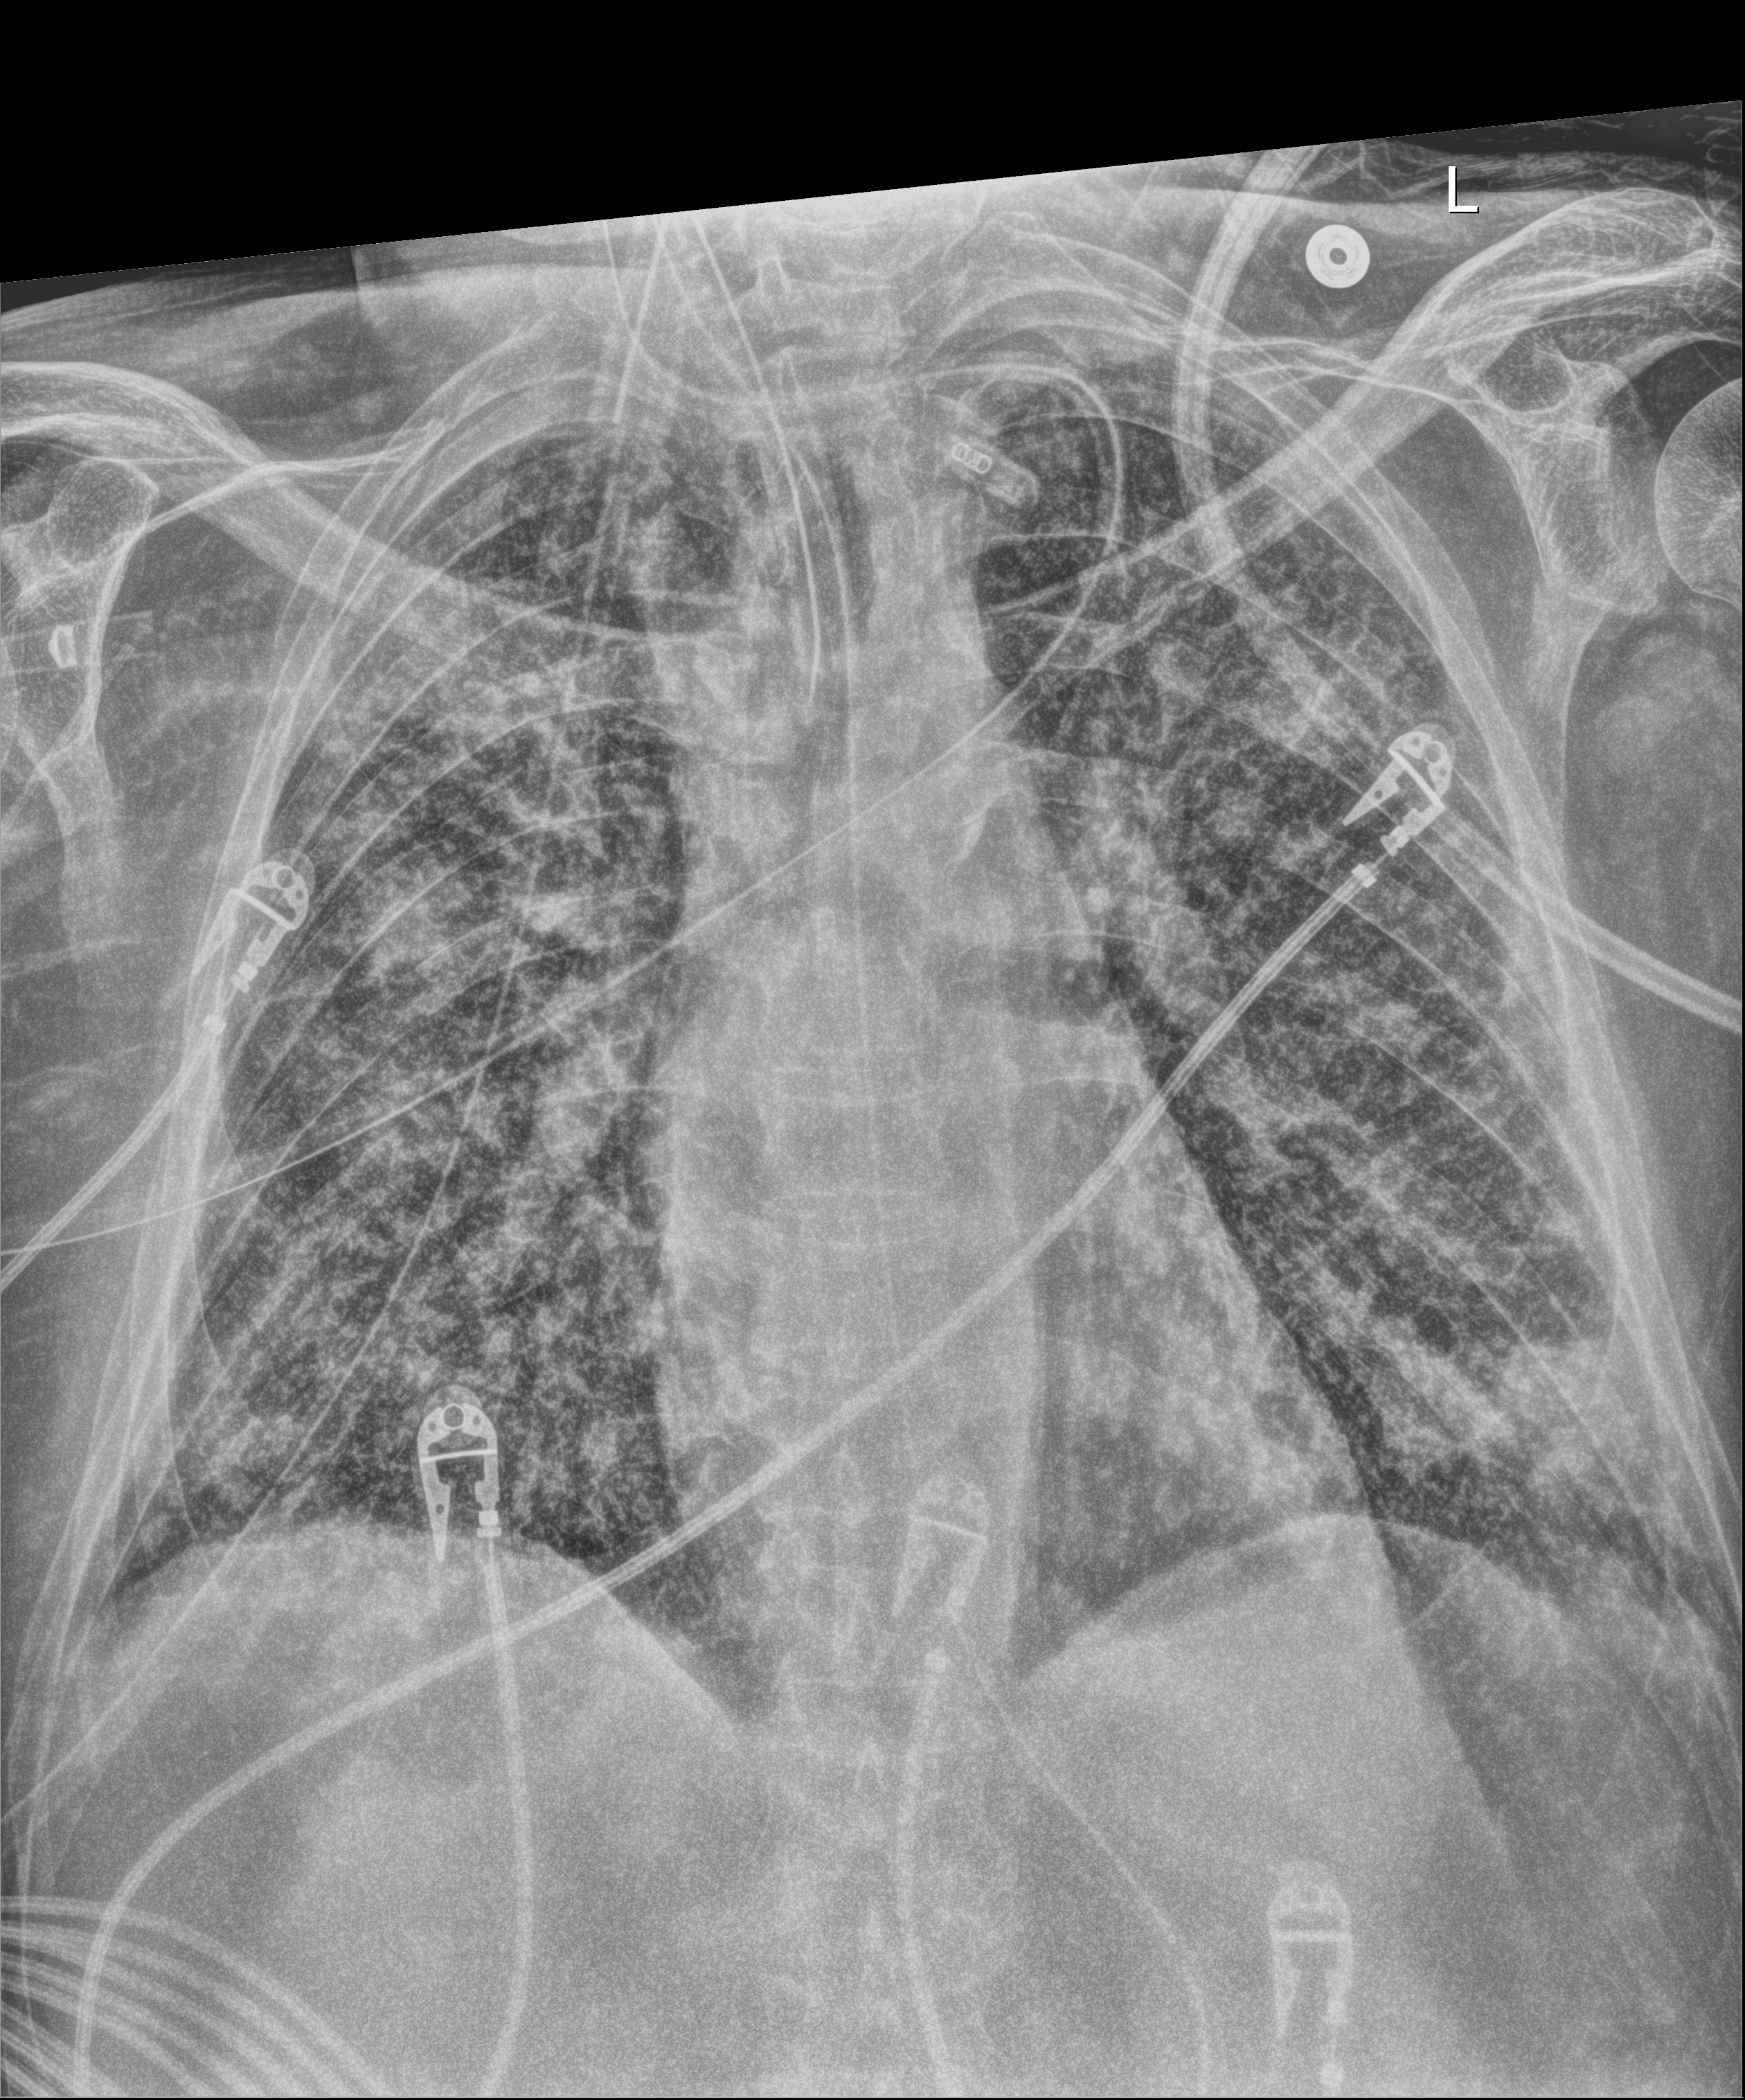
Chest X-ray (portable). Patient hospitalised with COVID-19; male, aged 60–74 years.
Hospital-stay facts (about this admission, not read from this image; timing relative to this image not recorded):
- admitted to intensive care during this hospital stay: yes
- mechanically ventilated during this hospital stay: yes
- chronic kidney disease (admission record): no